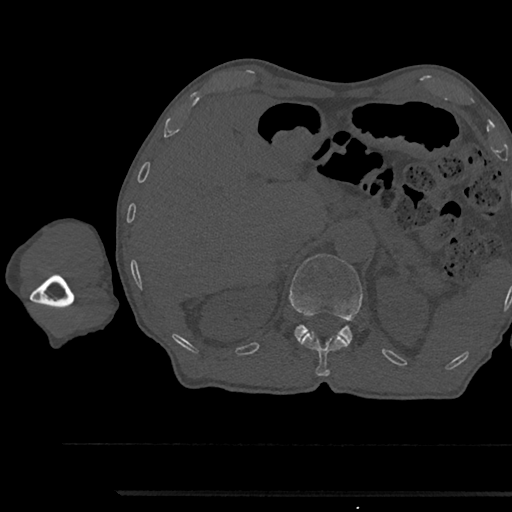
CT including the spine, one axial slice. Position 677 of 797 along the scan axis. 120 kVp. Bone window (W 1800 / L 400 HU). 0.5 mm slice thickness. 512 × 512 image matrix, field of view 367 × 367 mm. Male patient, age 79 years. From the clinical record (not read from this slice): primary cancer: prostate.
Annotated regions visible in this slice (semi-automatically segmented with operator editing):
- L1 vertebra: bounding box (x1, y1, x2, y2) in pixels: (290, 254, 362, 342)
- T12 vertebra: (299, 331, 350, 376)